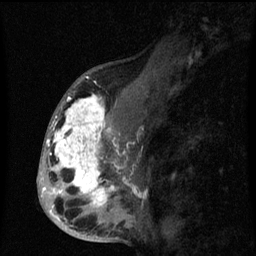
Breast MRI (dynamic contrast-enhanced), one sagittal slice; position 36 of 60 along the scan axis; dynamic contrast-enhanced series, image 2 of 3 at this slice position (ordered by acquisition); 1.5 T; TE 4.2 ms, TR 8 ms; 2 mm slice thickness; 256 × 256 image matrix, field of view 190 × 190 mm. Female patient, age 50 years.
Structures marked on this image (semi-automatic segmentation, software-assisted and operator-edited):
- analysis volume of interest (the breast-tissue region the enhancement analysis was run in; not a lesion): bounding box (x1, y1, x2, y2) in pixels: (43, 90, 141, 216)
- tumour enhancement mask (voxels above the 70 % enhancement threshold inside the analysis volume of interest): (43, 93, 138, 216)